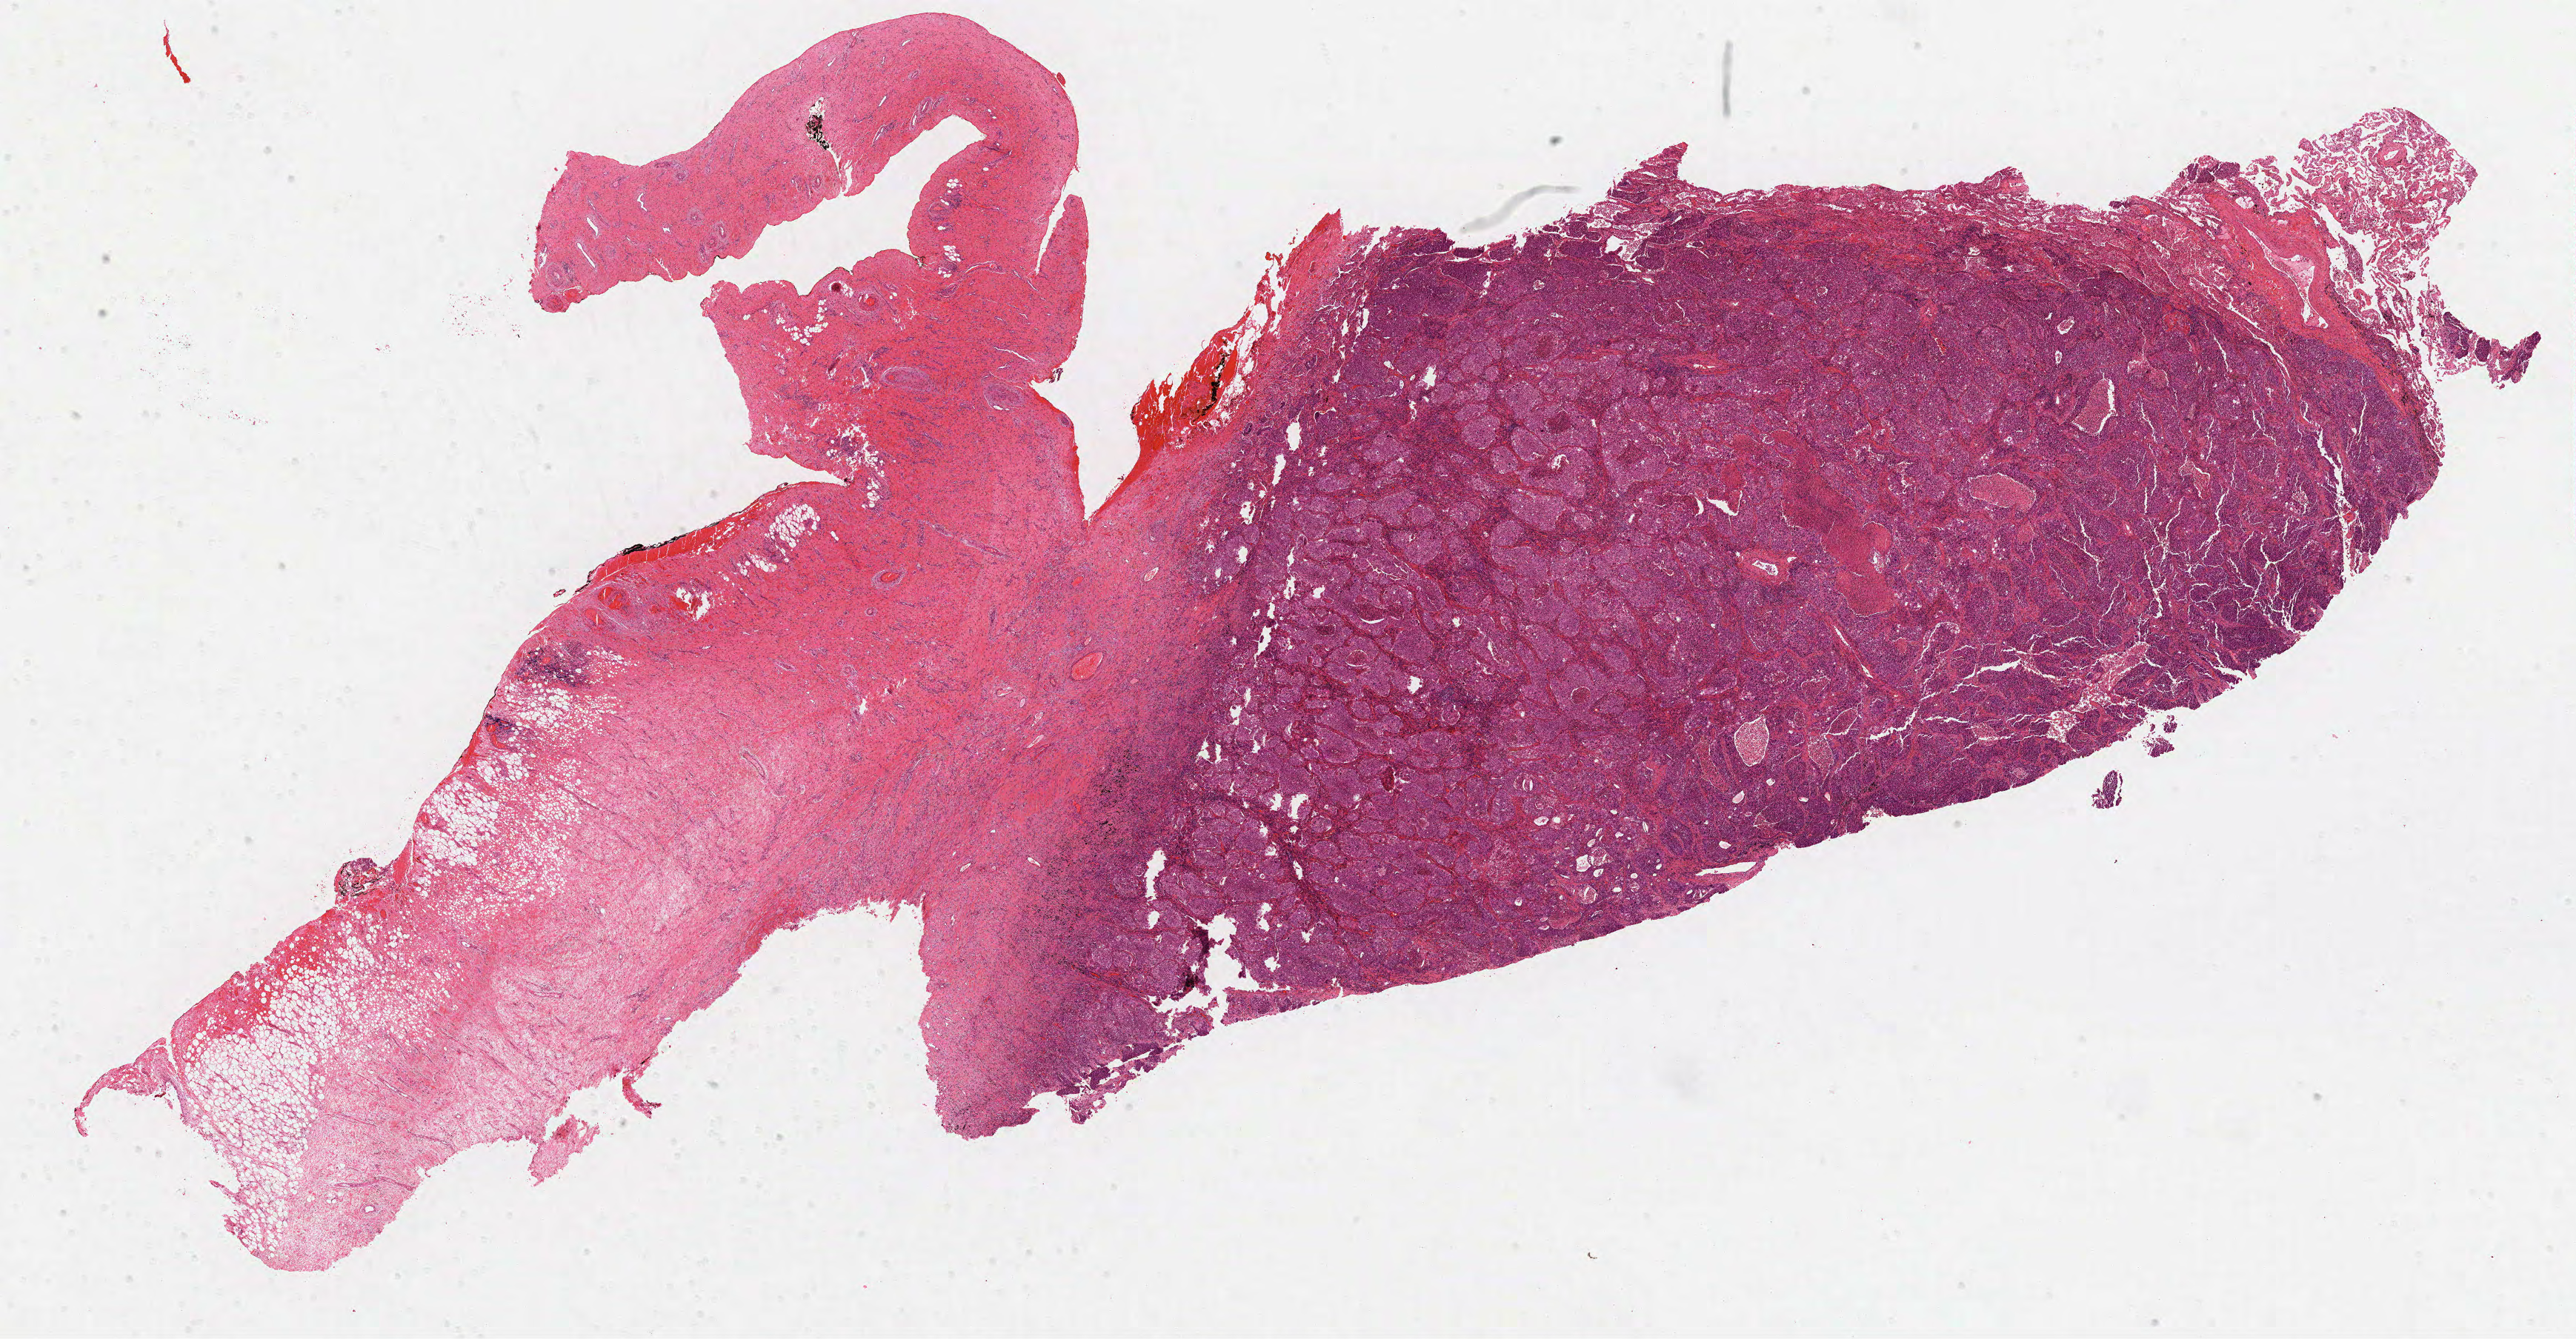
Digitized H&E tissue section (whole slide), low-resolution overview of the scanned area, about 28.0 x 14.6 mm (acquisition: 40x scan), formalin-fixed paraffin-embedded (FFPE) diagnostic section, sample: primary tumour, lung. Male patient; age at initial diagnosis 52 years.
AJCC pathologic stage: IIIA (7th edition). TNM: T2b N2 MX. Laterality: left. Diagnosis: Squamous cell carcinoma, NOS.